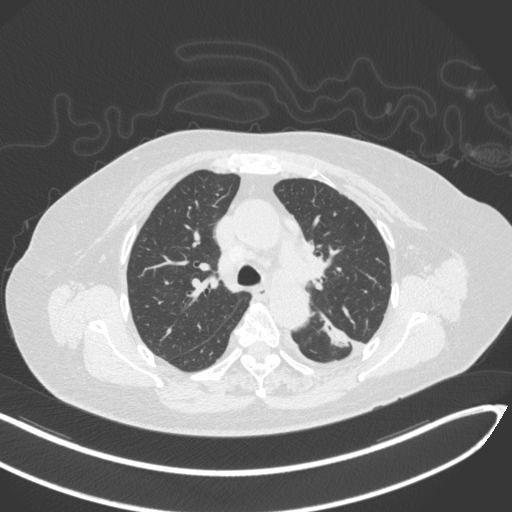
Chest CT, one axial slice. Position 216 of 270 along the scan axis. Reconstruction kernel B31f. Lung window (W 1500 / L -600 HU). 1 mm slice thickness. 512 × 512 image matrix. Female patient, age 76 years. Case-level facts recorded for this patient, not image findings: clinical TNM (as recorded): T1c N0 M0.
Structures marked on this image (rectangle marked by the reading radiologist):
- lung tumour (recorded histology: adenocarcinoma): box from (x=320, y=312) to (x=356, y=350) px